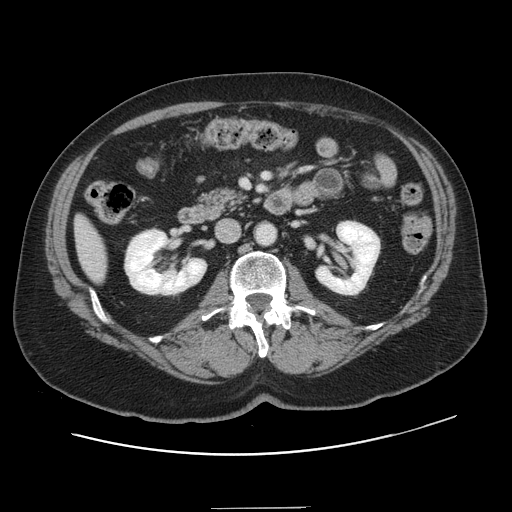
Contrast-enhanced abdominal CT, one axial slice; slice 49 of 143 in the series (ordered by position); 120 kVp; intravenous contrast given; soft-tissue window (W 400 / L 40 HU); 512 × 512 image matrix. Male patient, age 62 years. Case-level facts recorded for this patient, not image findings: diagnosis: colorectal cancer liver metastases, imaged before liver resection; multiple liver metastases: yes; largest metastasis: 2.7 cm; disease in both lobes: no.
Outlined on this slice (manually delineated by an expert):
- liver: bounding box (x1, y1, x2, y2) in pixels: (76, 219, 106, 280)